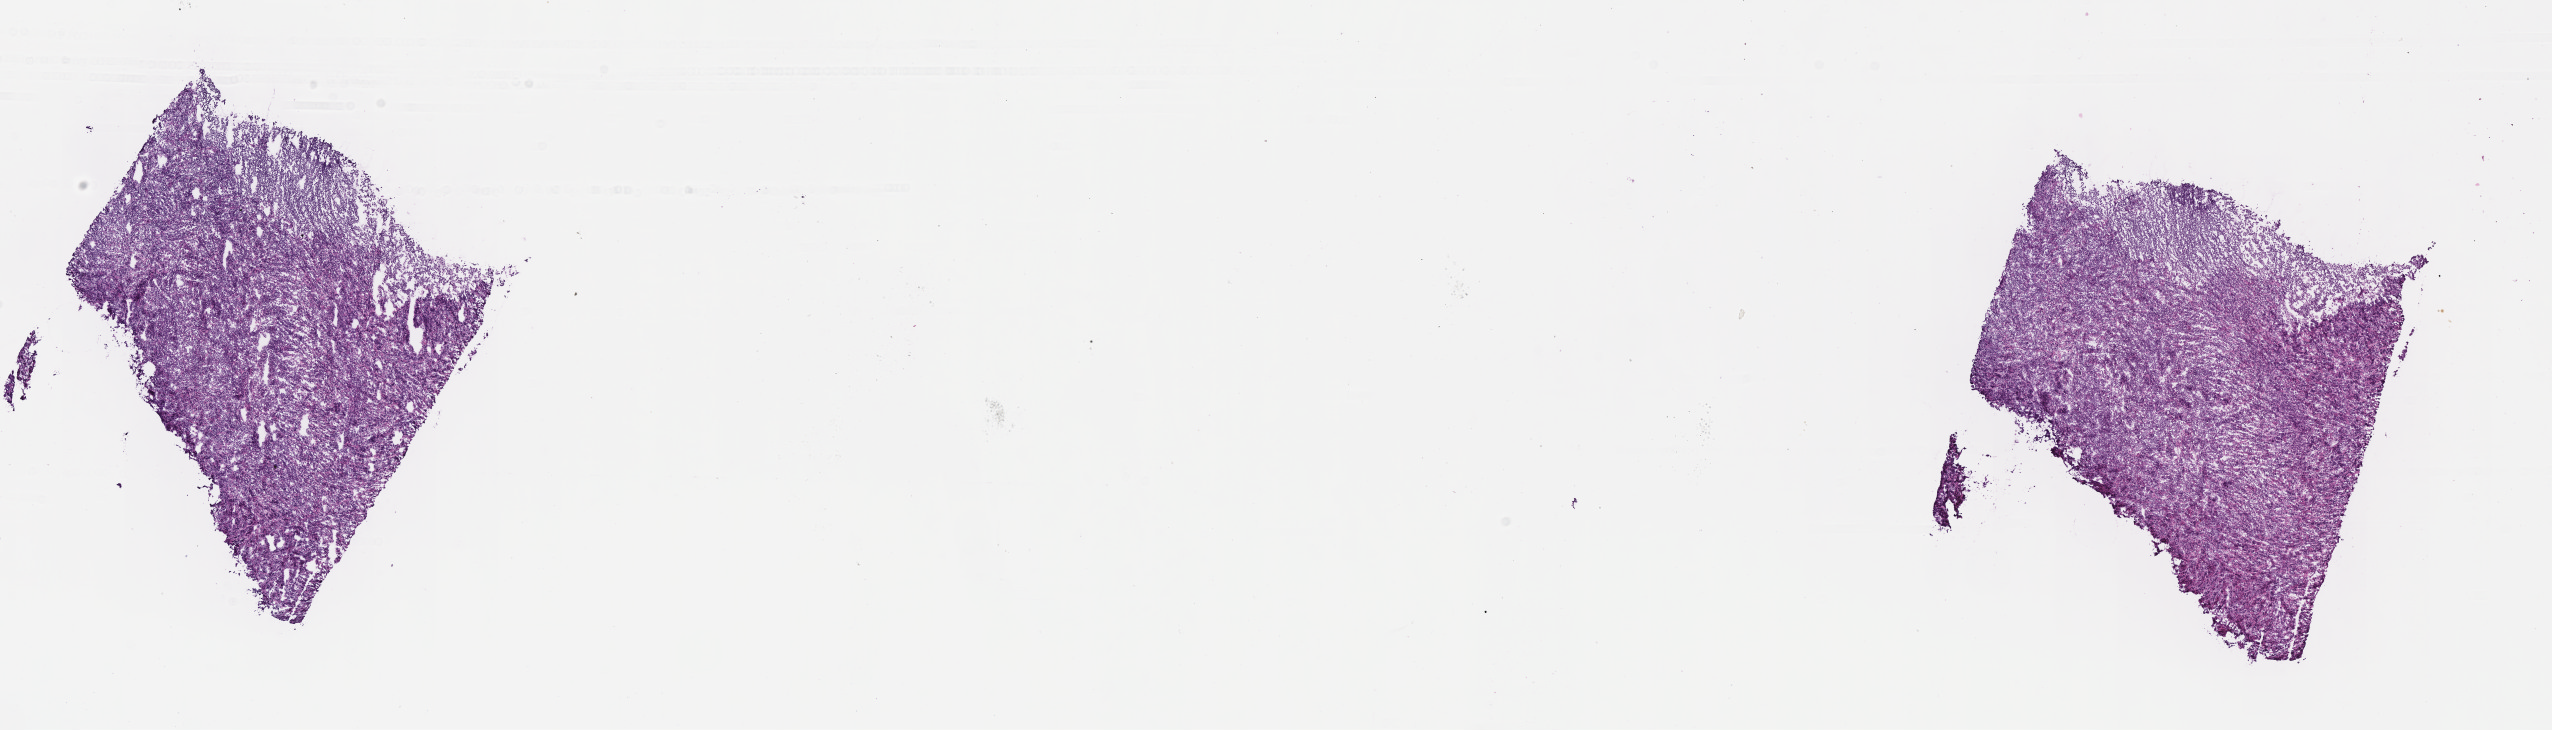
H&E whole-slide image — a low-resolution overview of the entire scanned area, about 20.6 x 5.9 mm, cryosection, primary tumor, site: soft tissue. Female patient; age at initial diagnosis 9 years. Composition of this section per pathologist review: tumor cells 90%, tumor nuclei 95%, stromal cells 5%, necrosis 5%, normal cells 0%. Infiltration values recorded for this section: lymphocyte infiltration 3%, monocyte infiltration 3%, neutrophil infiltration 0%.
Diagnosis: Burkitt lymphoma, NOS. Ann Arbor stage (patient): Stage III. Section: top of the tissue portion.